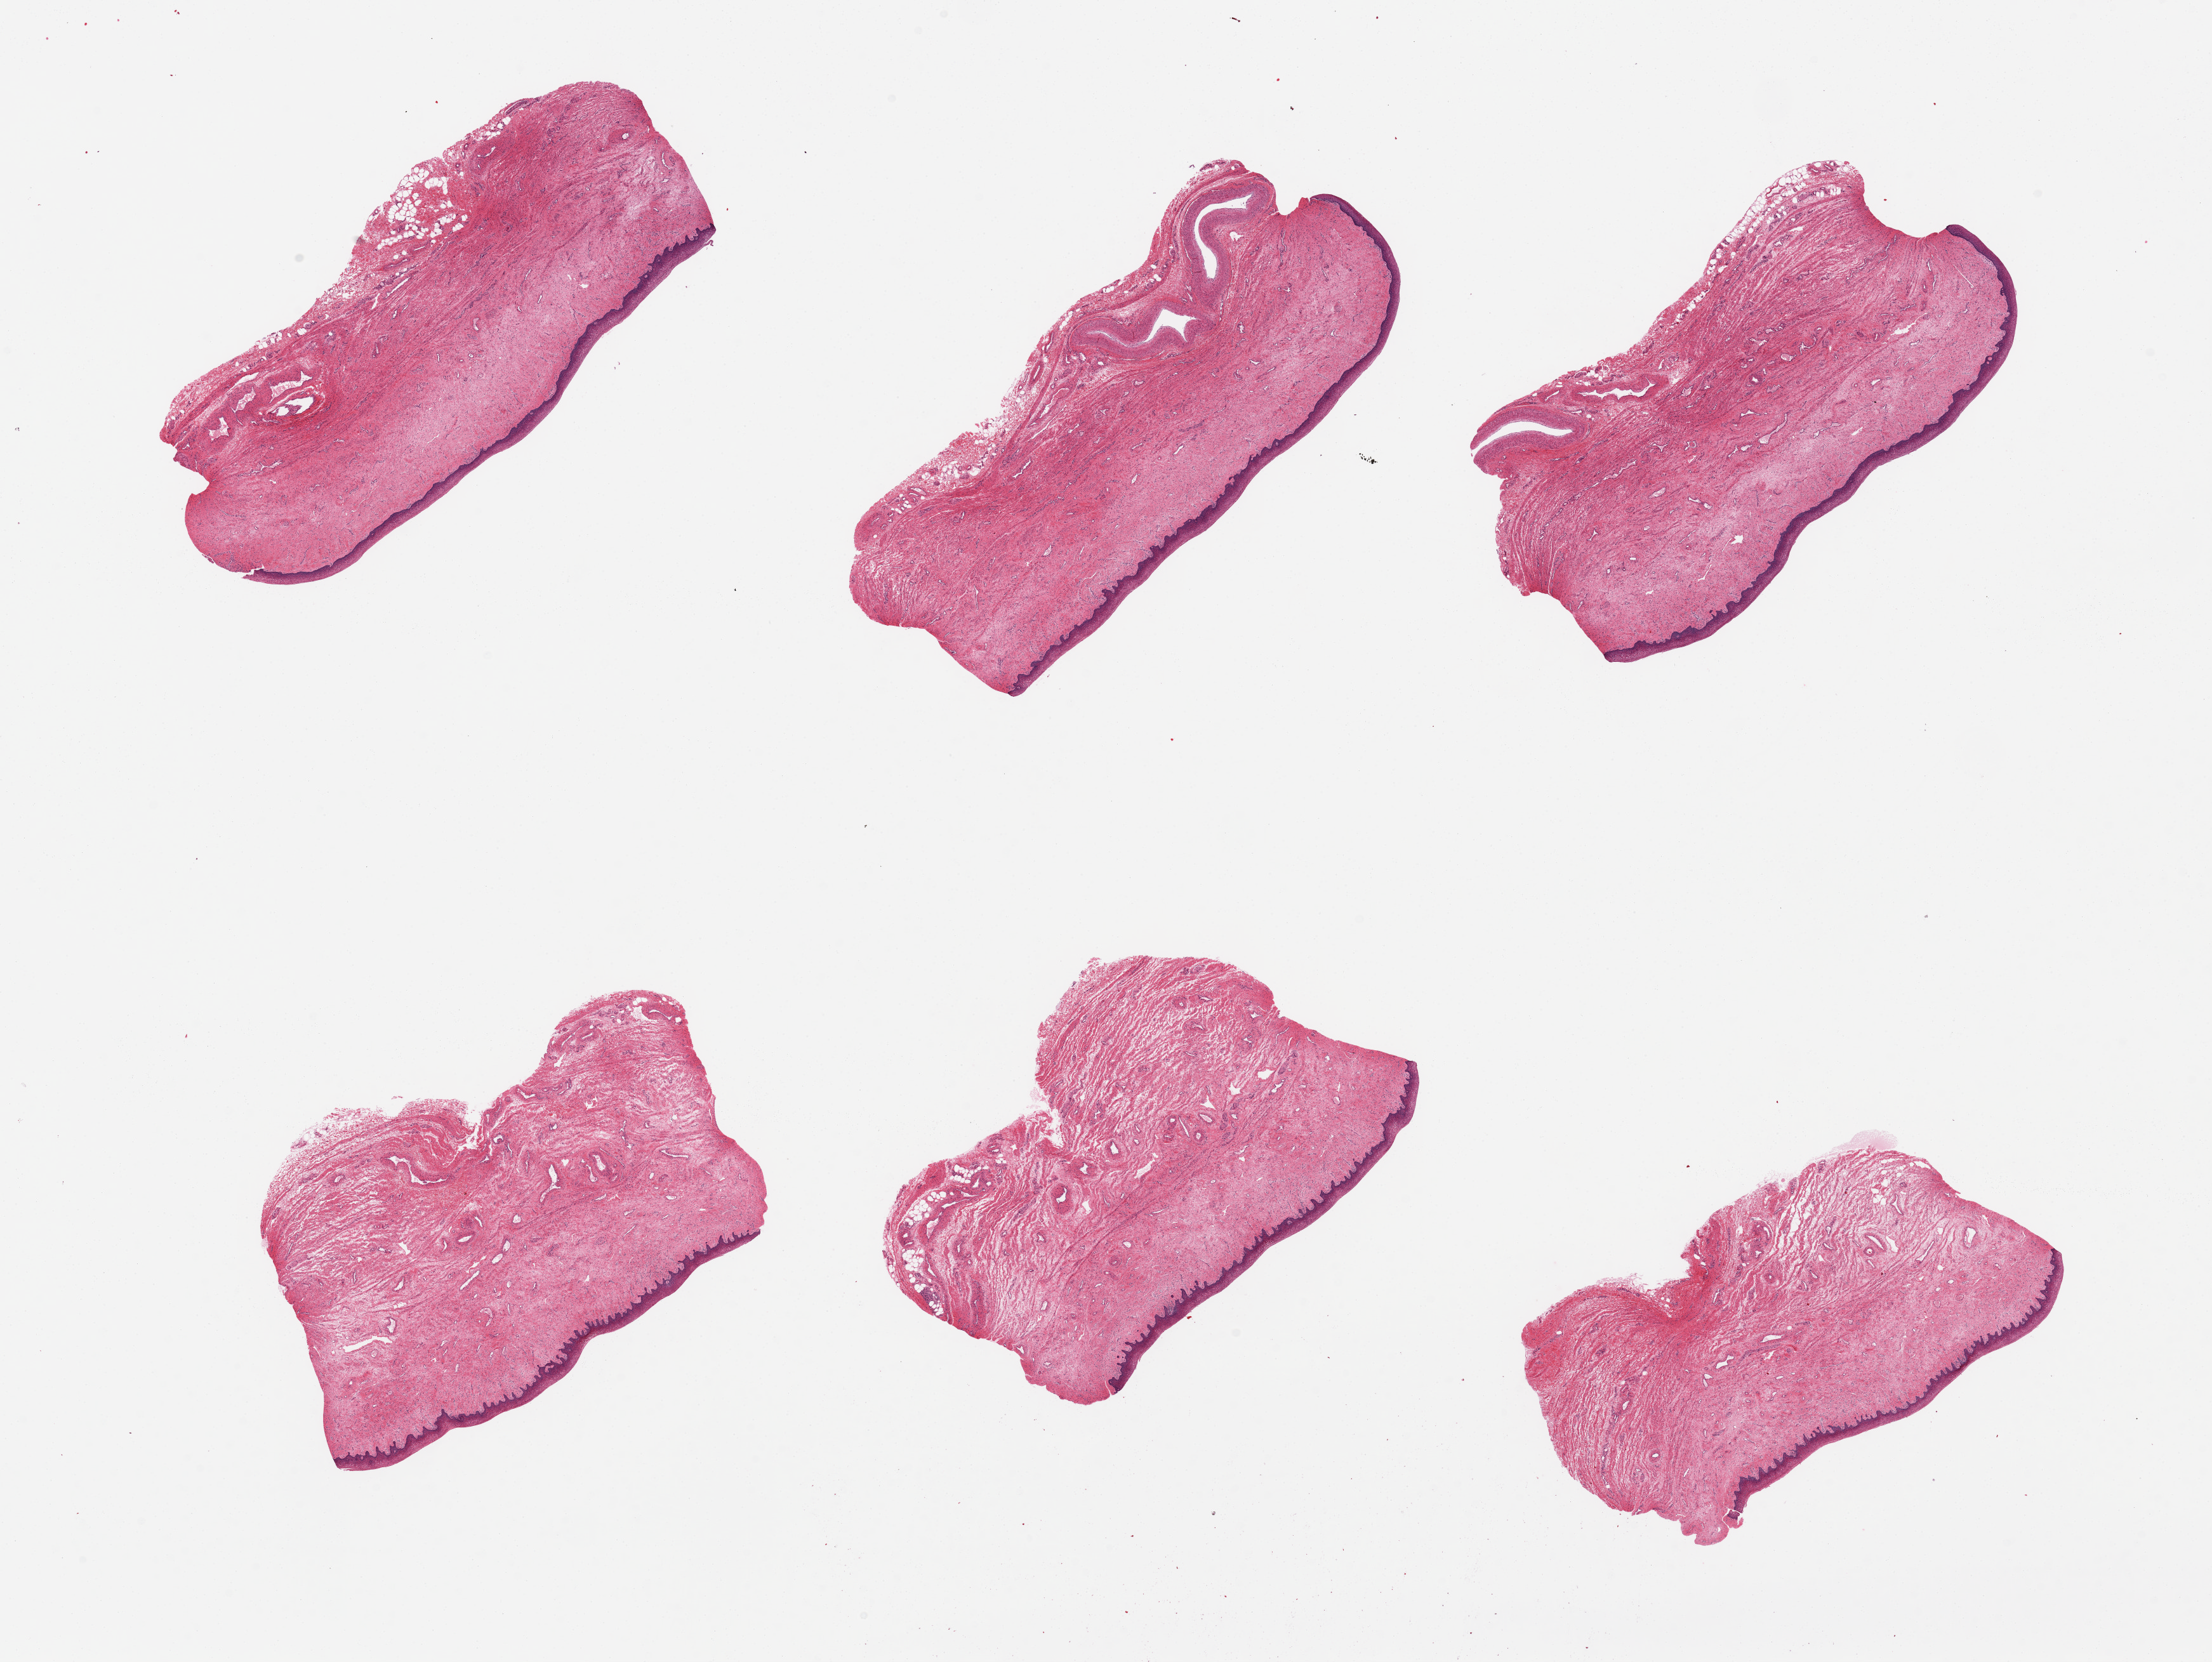
Whole-slide image, hematoxylin and eosin (H&E) stain, low-resolution overview of the scanned area, about 27.6 x 20.7 mm. PAXgene-fixed paraffin-embedded (PFPE) section. Section of vagina (target tissue). Donor tissue sample. Donor sex: female.
Reviewer comment on this tissue sample: 6 pieces, squamous mucosa well preserved, ~0.2mm, 5-10% thickness.